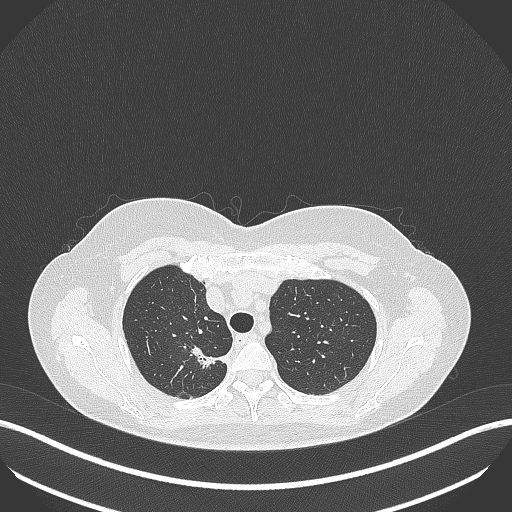
Chest CT, one axial slice. Slice 314 of 386 in the series (ordered by position). 120 kVp. Lung window (W 1500 / L -600 HU). 512 × 512 image matrix, field of view 400 × 400 mm. Female patient, age 65 years. From the clinical record (not read from this slice): clinical TNM (as recorded): T1b N0 M0.
Outlined on this slice (bounding box drawn by a radiologist):
- lung tumour (recorded histology: adenocarcinoma): bounding box [x1, y1, x2, y2] px = [187, 343, 226, 374]